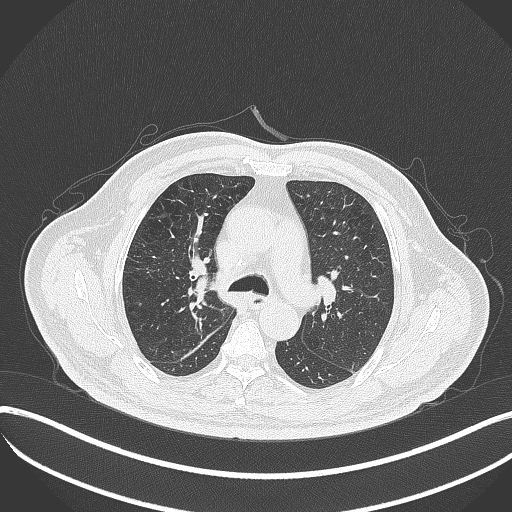
Chest CT, one axial slice; position 241 of 401 along the scan axis; reconstruction kernel B70f; lung window (W 1500 / L -600 HU); 1 mm slice thickness; 512 × 512 image matrix. Patient: male, 72 years. From the clinical record (not read from this slice): clinical TNM (as recorded): T1c N0 M0; histopathological grade: G2.
Structures marked on this image (bounding box drawn by a radiologist):
- lung tumour (recorded histology: squamous cell carcinoma): bounding box [x1, y1, x2, y2] px = [186, 258, 213, 300]